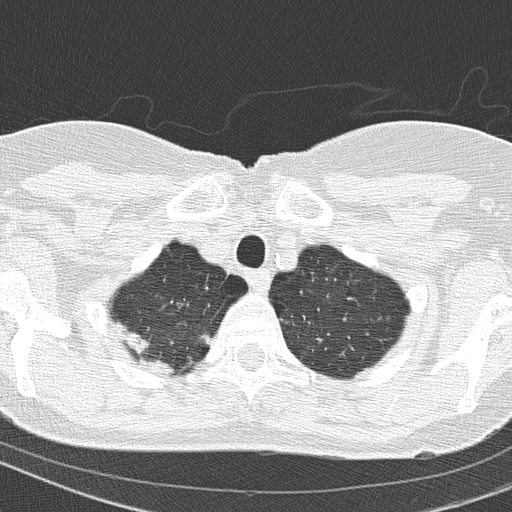
Low-dose screening chest CT, one axial slice. Position 137 of 154 along the scan axis. 120 kVp. Lung window (W 1500 / L -600 HU). 512 × 512 image matrix, field of view 288 × 288 mm.
Annotated regions visible in this slice (manually delineated by an expert):
- lesion 1 (tumor, upper lobe of right lung): bounding box (x1, y1, x2, y2) in pixels: (142, 358, 174, 374)